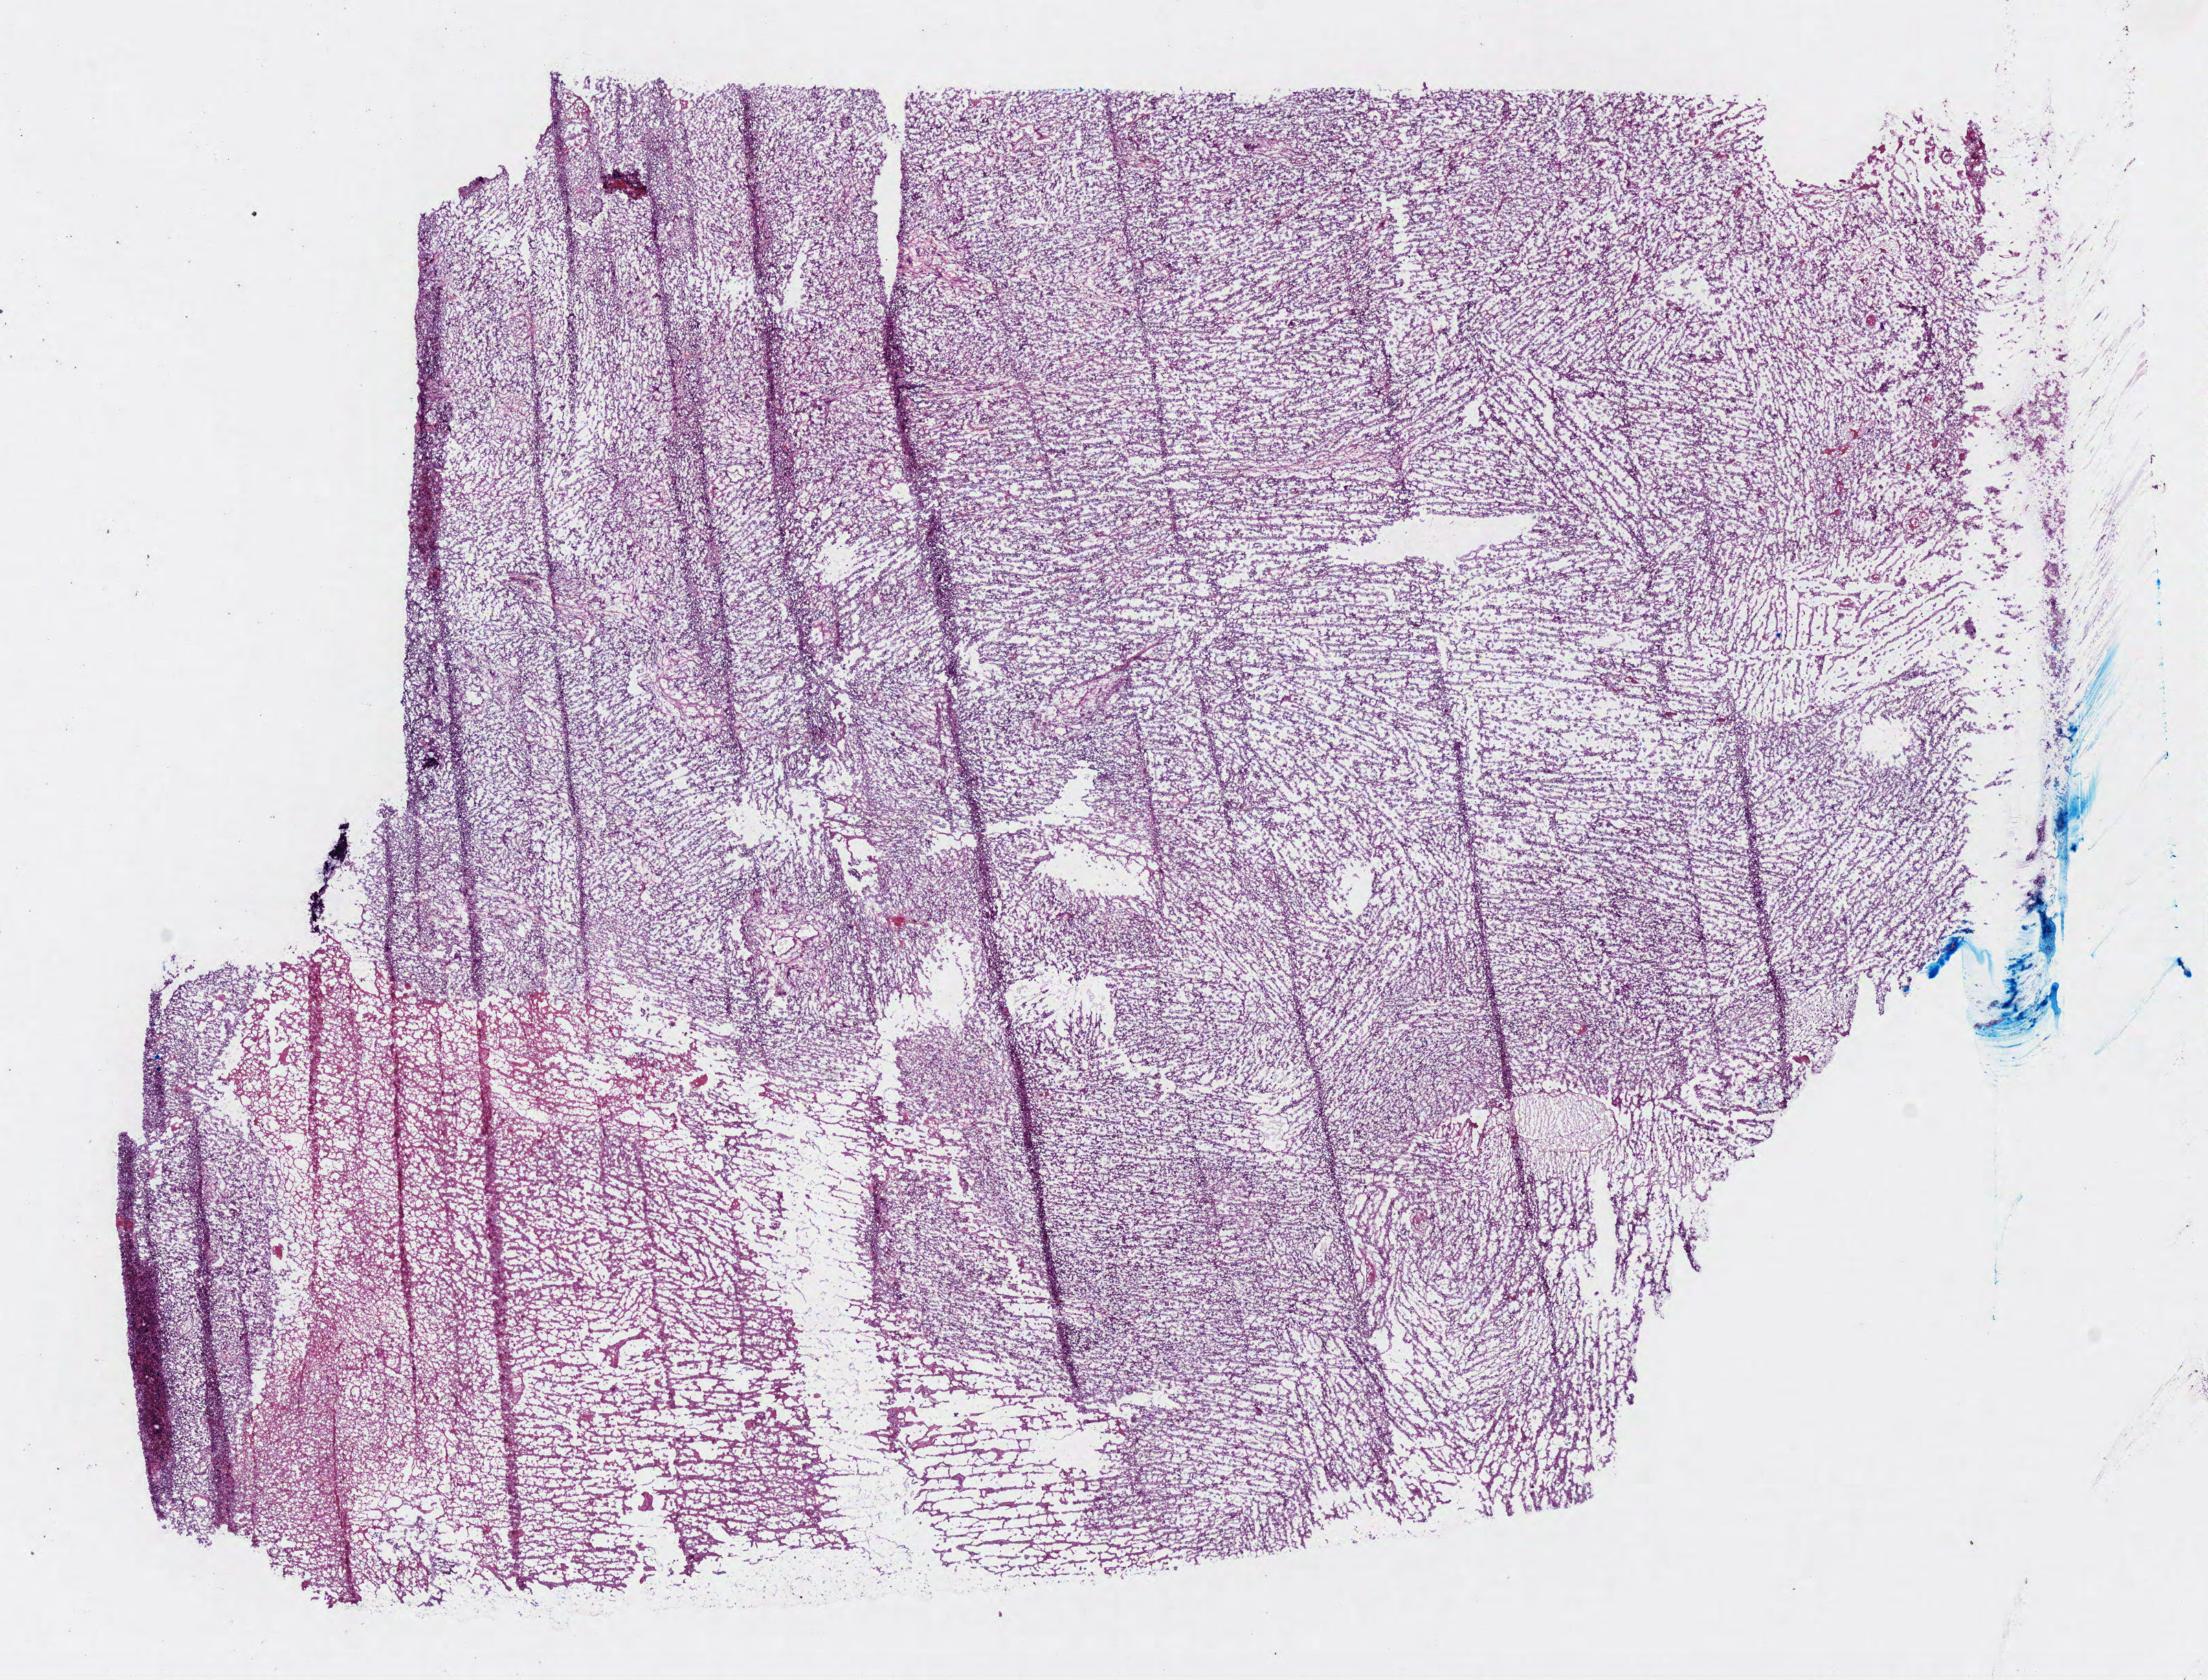
Whole-slide histology image, Hematoxylin and eosin (H&E) stained — low-resolution overview of the scanned area, about 12.7 x 9.6 mm (slide scanned at 40x), frozen section from the bottom of the tissue portion, brain, primary tumour sample. Female patient; age at initial diagnosis 72 years. Slide review estimates, as recorded: tumour cells 90%, tumour nuclei 80%, normal cells 0%, stromal cells 0%, necrosis 10%.
Pathologic diagnosis: Glioblastoma.